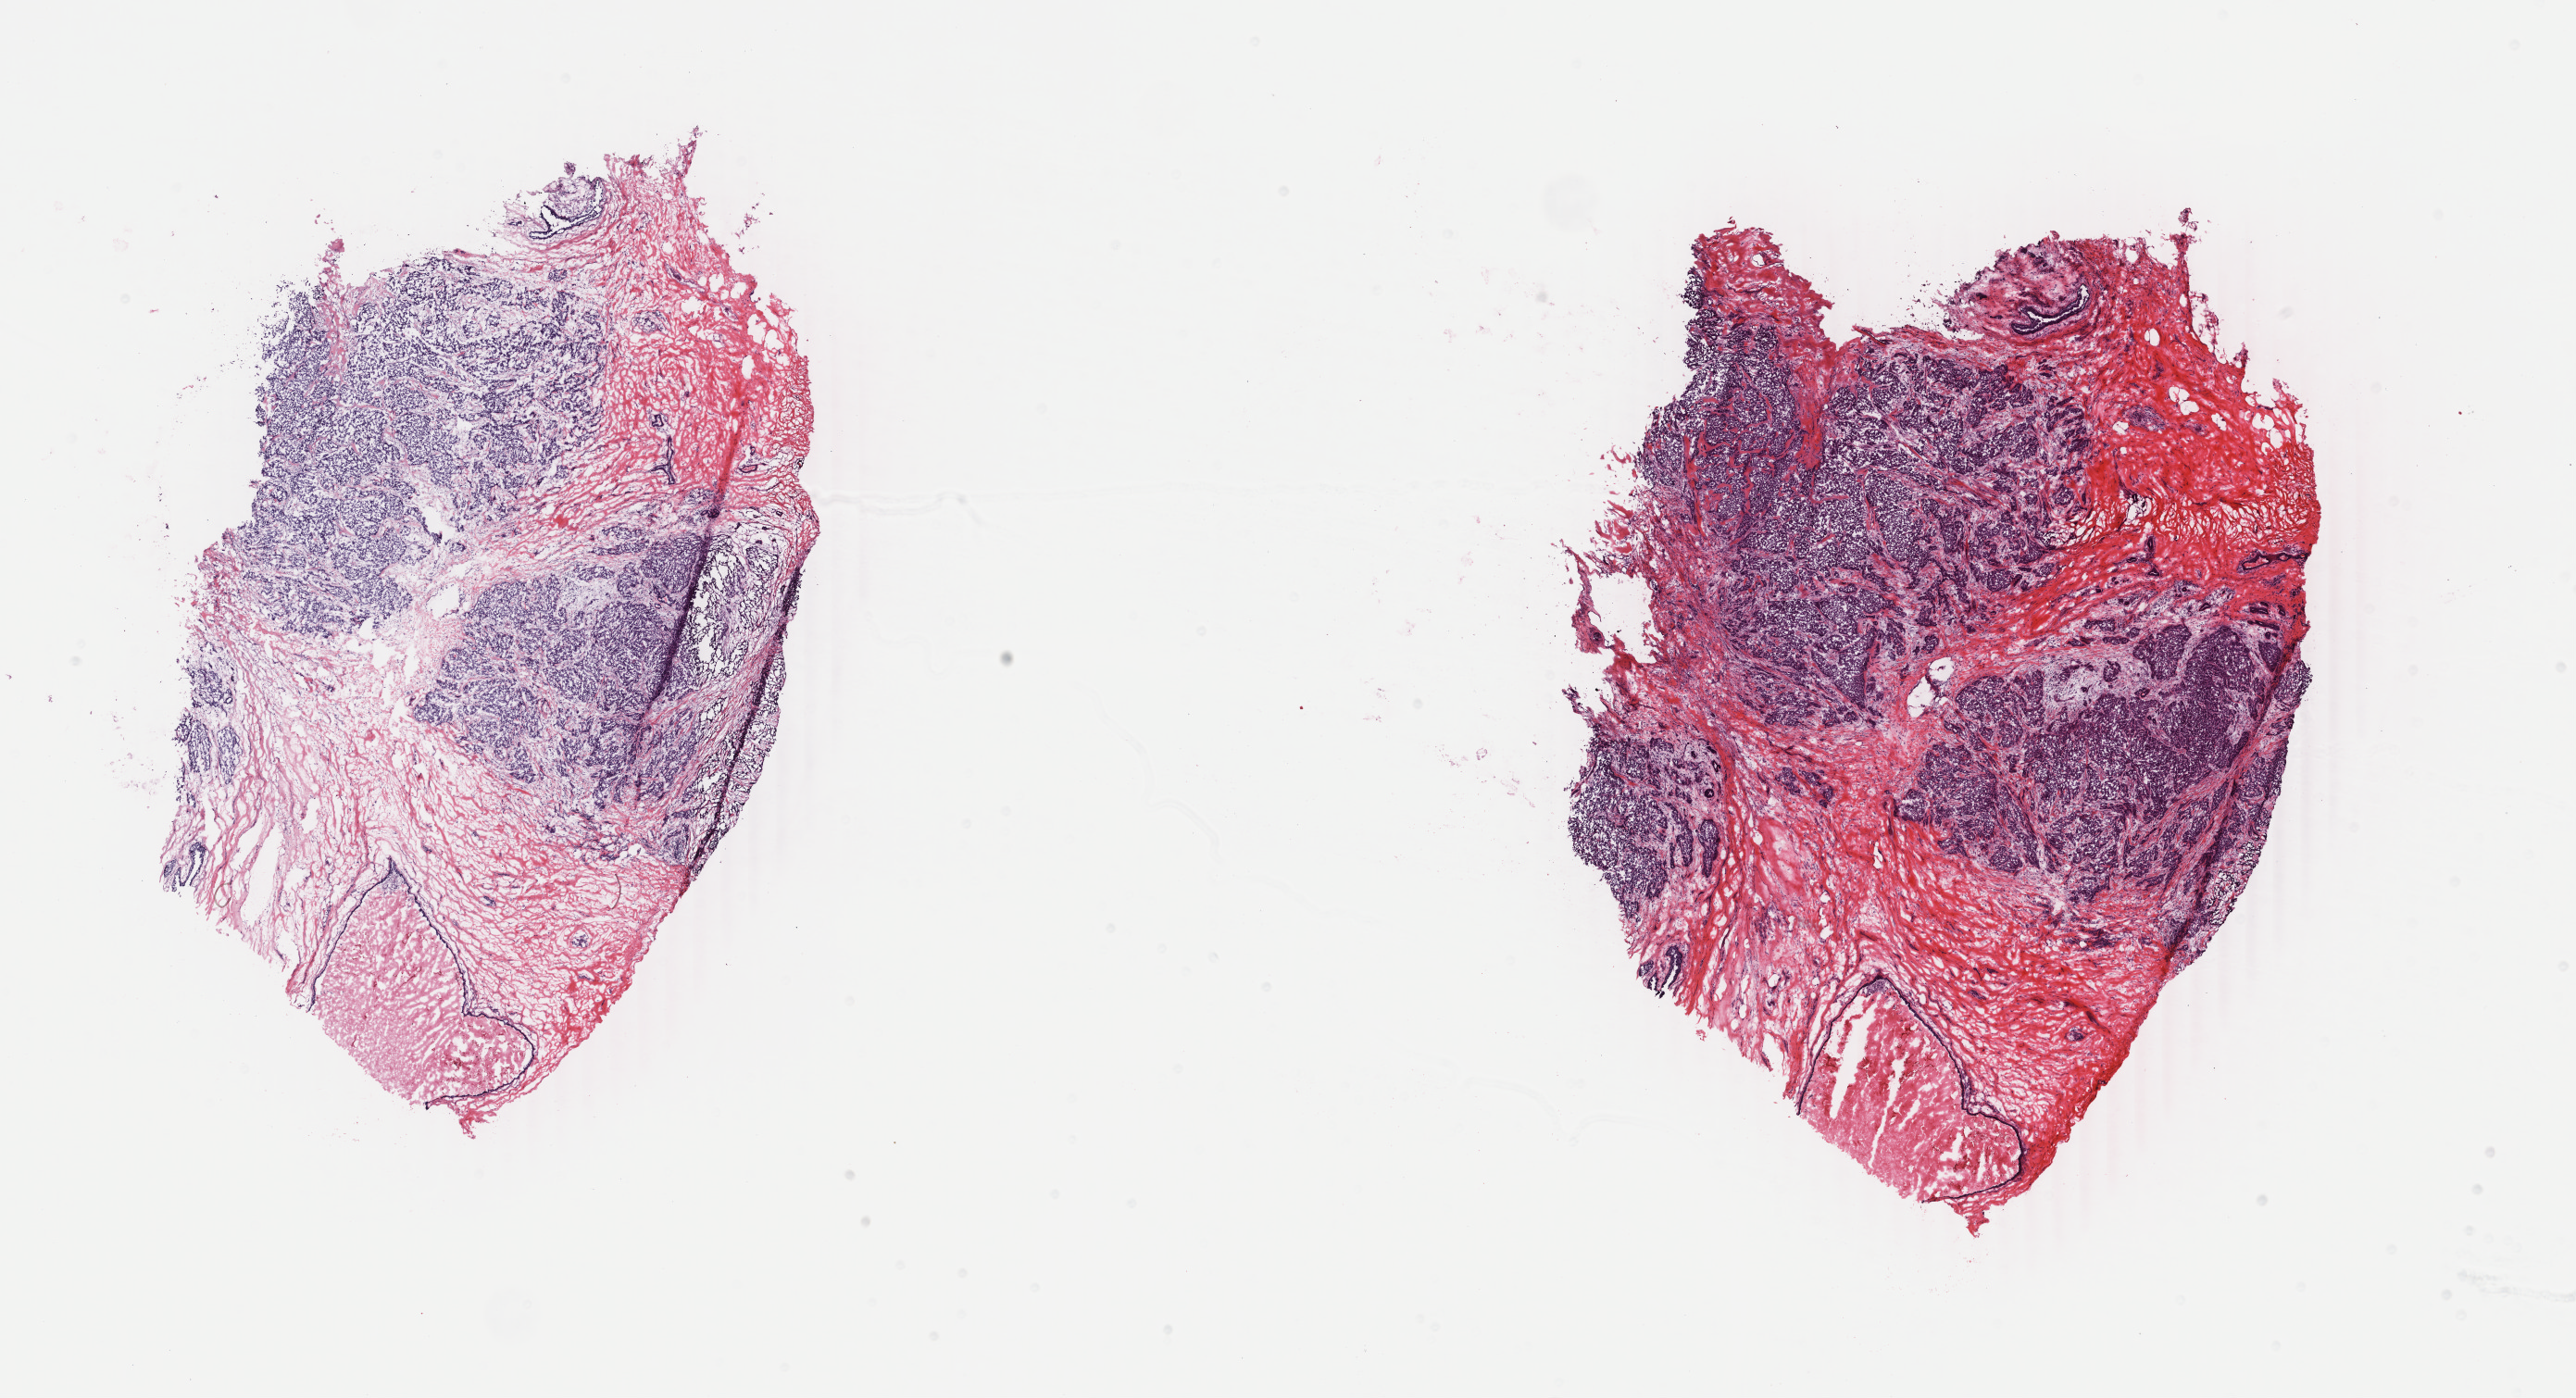
Digitized H&E-stained tissue section (whole slide), a low-resolution overview of the entire scanned area, about 22.1 x 12.0 mm, frozen section, sample: primary tumour, breast. Female patient; age at initial diagnosis 66 years. Slide review estimates, as recorded: tumour cells 60%, tumour nuclei 90%.
Pathologic diagnosis: Infiltrating duct carcinoma, NOS.